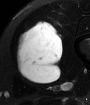
MRI of an extremity soft-tissue mass, one axial slice. Slice 24 of 65 in the series (ordered by position). T2-weighted fat-saturated. MR volume resampled by the dataset authors to the PET/CT grid (not the native acquisition matrix). 90 × 105 image matrix. Male patient. From the clinical record (not read from this slice): histological type: mixoid liposarcoma; grade: low; site of the primary tumour: left thigh.
Structures marked on this image (expert contour drawn on MRI and transferred to this co-registered scan by the dataset authors):
- gross tumour volume (mass): bounding box (x1, y1, x2, y2) in pixels: (16, 21, 63, 83)